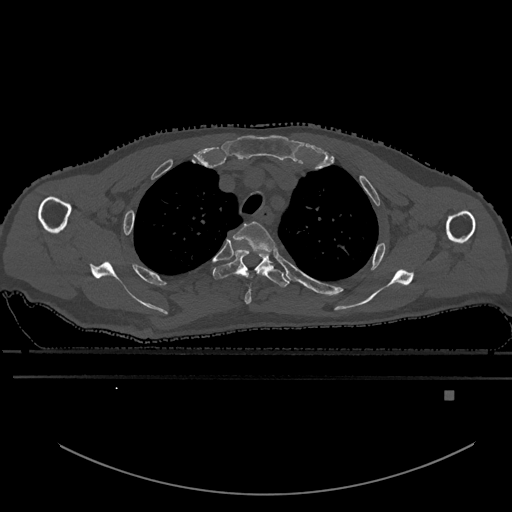
CT including the spine, one axial slice; slice 467 of 969 in the series (ordered by position); bone window (W 1800 / L 400 HU); 512 × 512 image matrix, field of view 456 × 456 mm. Patient: male, 82 years. Case-level facts recorded for this patient, not image findings: primary cancer: prostate; vertebrae with lytic lesions (as recorded): T11, T9, T8, T2.
Structures marked on this image (semi-automatic segmentation, software-assisted and operator-edited):
- T2 vertebra: bounding box [x1, y1, x2, y2] px = [233, 221, 275, 305]
- T3 vertebra: [213, 250, 289, 287]